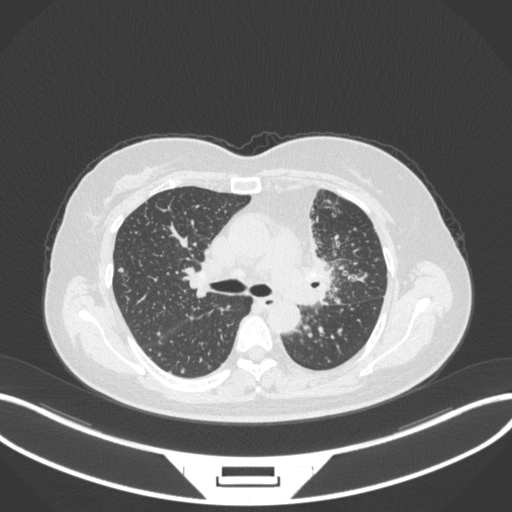
Chest CT, one axial slice; slice 211 of 348 in the series (ordered by position); reconstruction kernel B31f; lung window (W 1500 / L -600 HU); 1 mm slice thickness; 512 × 512 image matrix, field of view 400 × 400 mm. Patient: female, 49 years. Case-level facts recorded for this patient, not image findings: clinical TNM (as recorded): T1c N0 M1.
Annotated regions visible in this slice (bounding box drawn by a radiologist):
- lung tumour (recorded histology: adenocarcinoma): bounding box <293,218,340,314> (left, top, right, bottom; pixels)